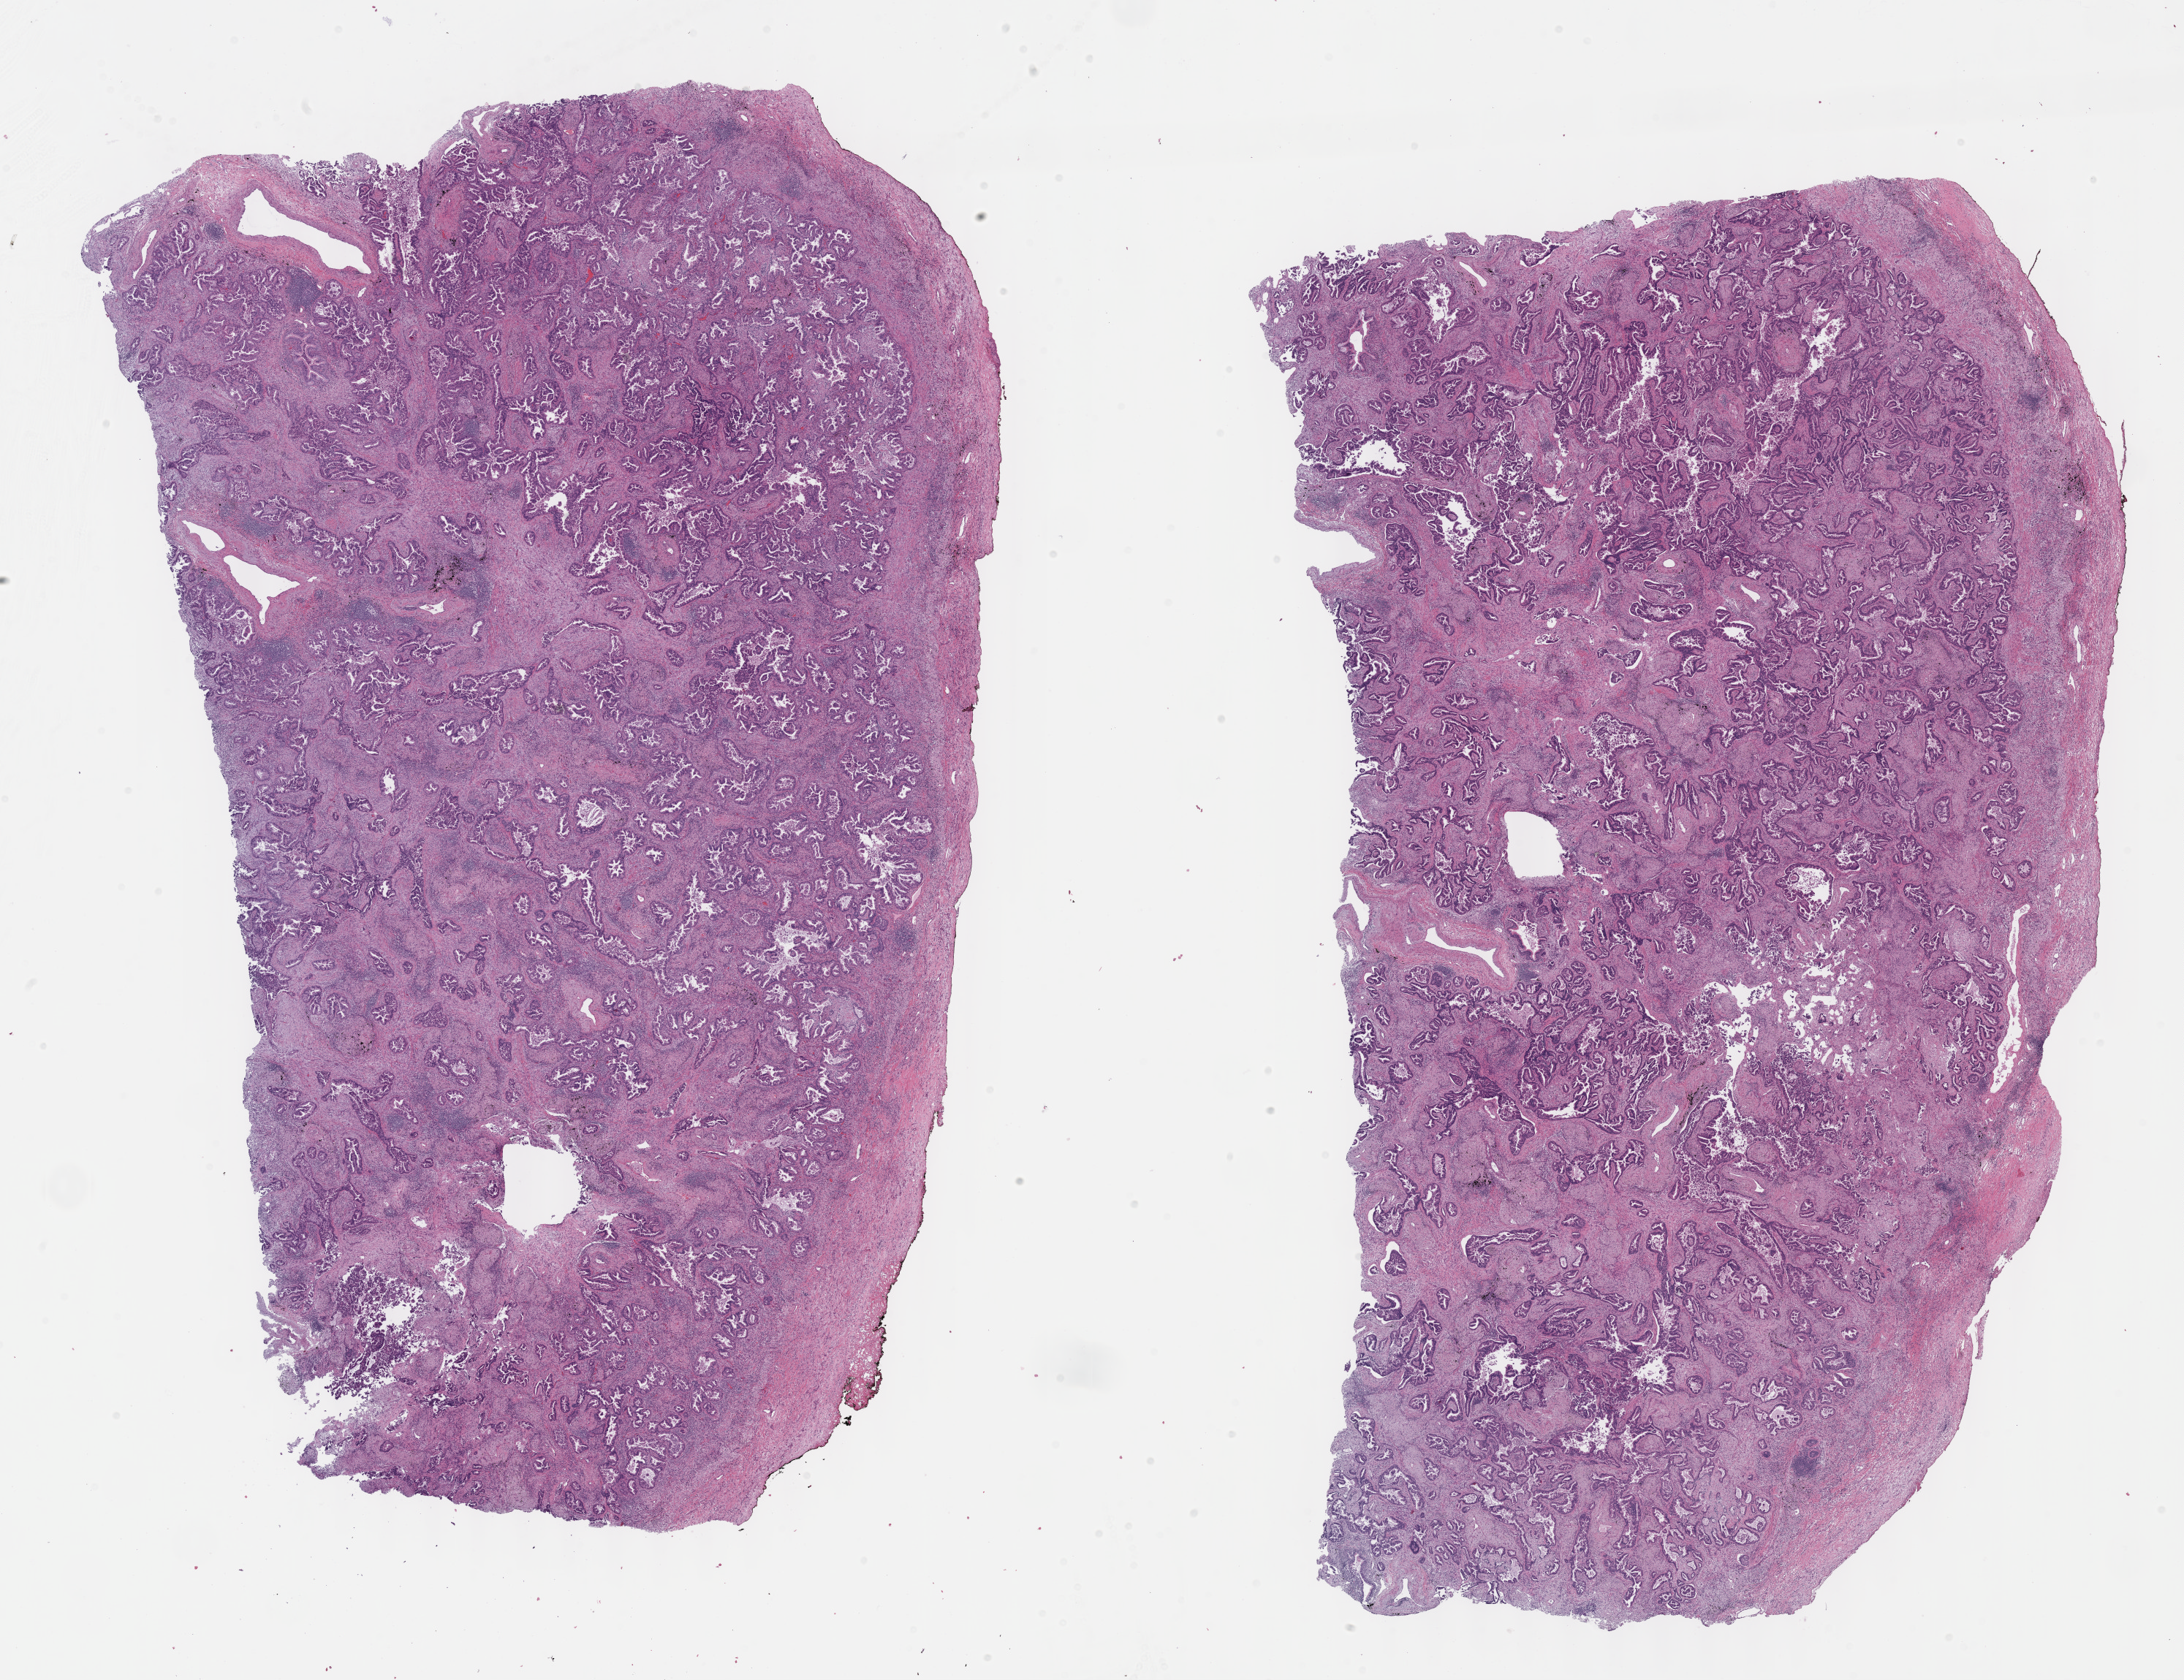
Whole-slide histology image, Hematoxylin and eosin (H&E) stained — low-resolution overview of the scanned area, about 24.1 x 18.6 mm (slide scanned at 40x), formalin-fixed paraffin-embedded (FFPE) diagnostic section, lung, primary tumour sample. Patient: male, age at initial diagnosis 71 years.
Pathologic diagnosis: Adenocarcinoma, NOS. AJCC pathologic stage: IIIA (6th edition). Laterality: left.